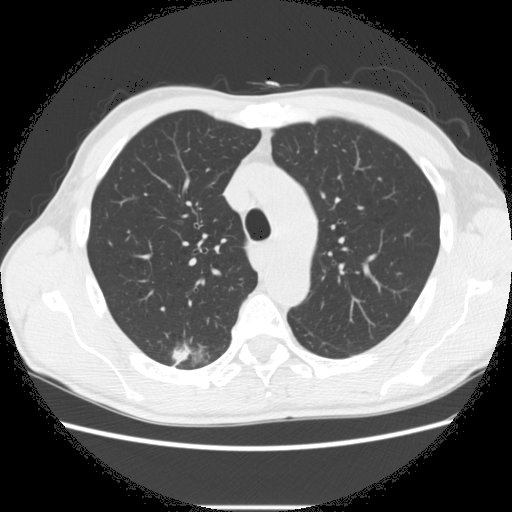
Low-dose screening chest CT, one axial slice; position 206 of 282 along the scan axis; reconstruction kernel STANDARD; 120 kVp; lung window (W 1500 / L -600 HU); 2.5 mm slice thickness; 512 × 512 image matrix, field of view 360 × 360 mm.
Structures marked on this image (expert manual segmentation):
- lesion 1 (tumor, upper lobe of right lung): bounding box [x1, y1, x2, y2] px = [171, 345, 189, 366]